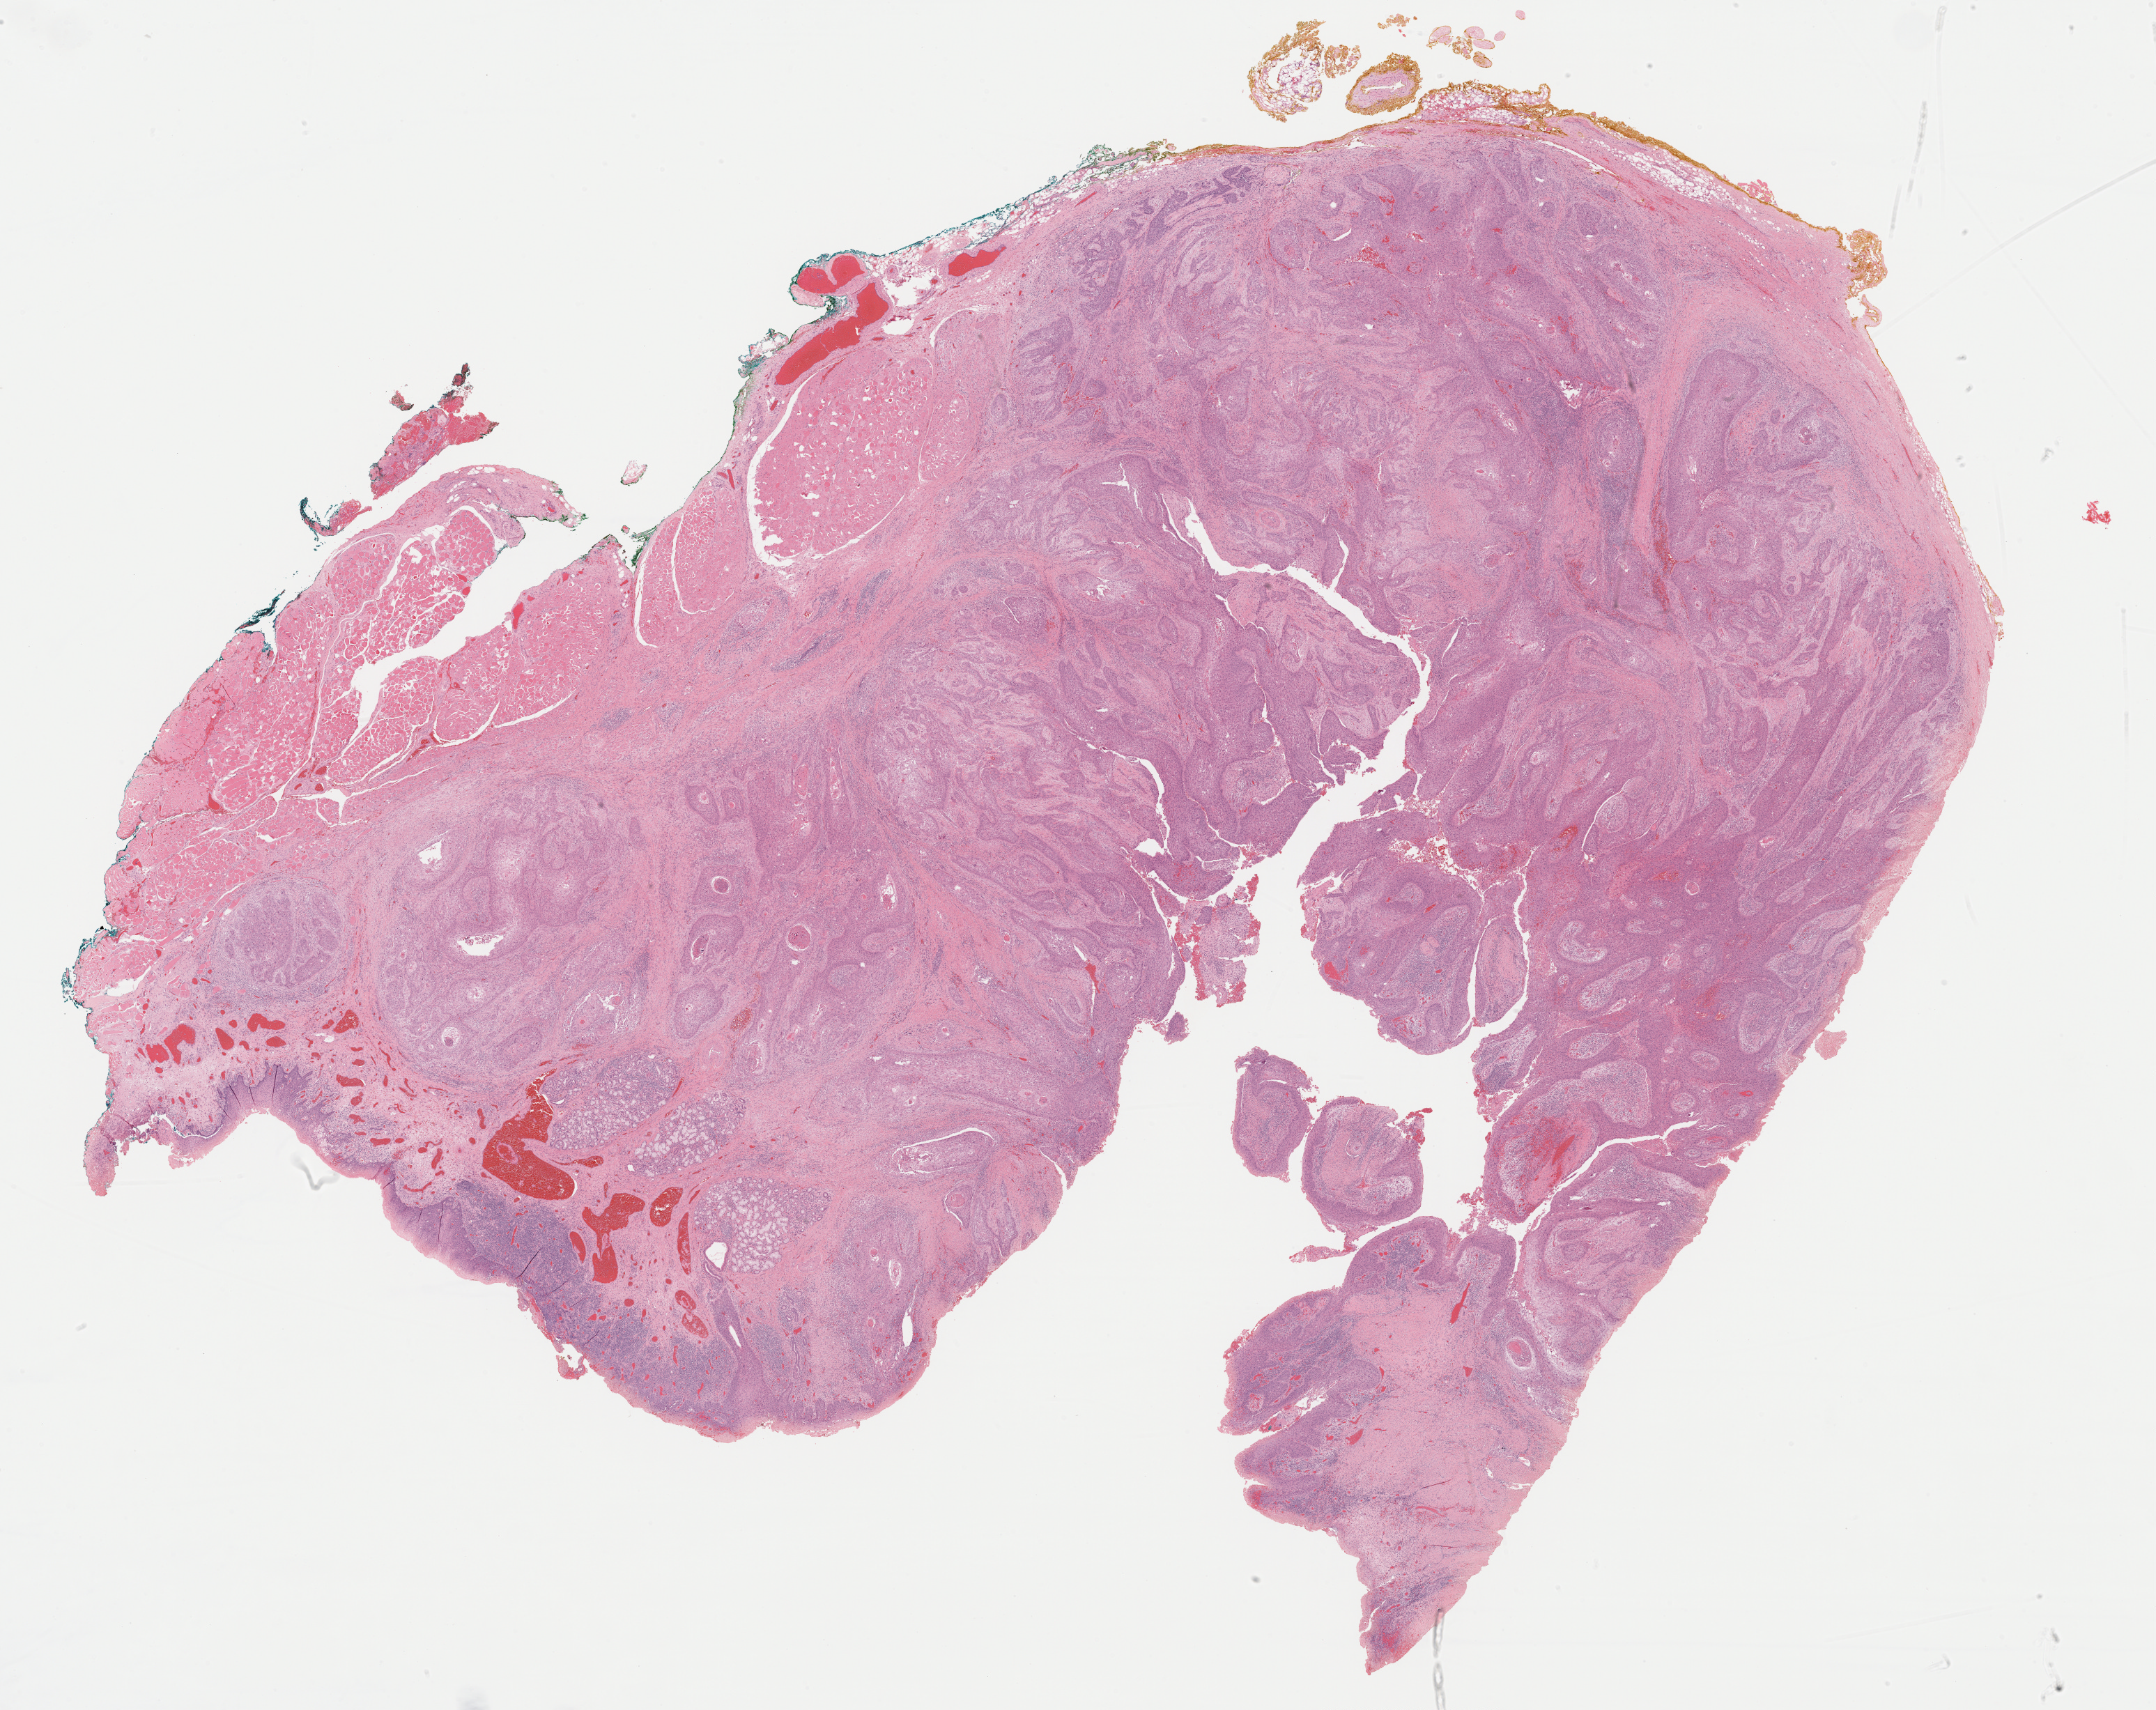
Whole-slide histology image, H&E-stained — shown as a low-resolution overview of the whole scanned area (about 24.4 x 19.3 mm, from a 40x scan); formalin-fixed paraffin-embedded (FFPE) diagnostic section; sample: primary tumour, head and neck. Male patient; age at initial diagnosis 49 years. Histologic grade: G3 (poorly differentiated).
Diagnosis: Squamous cell carcinoma, NOS (tonsil, NOS). AJCC pathologic stage: IVA (6th edition). Lymph nodes positive (case pathology): 4 of 35 examined.